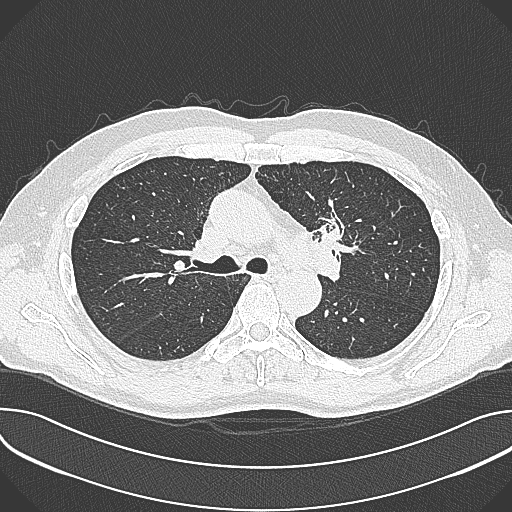
Low-dose screening chest CT, axial slice. First (baseline) screen. Lung window (W 1500 / L -600 HU). Lung (sharp) reconstruction kernel (B80f). Slice 116 of 361 in the series. 512 × 512 image matrix. Male participant, aged 59 years at enrolment. Current smoker at enrolment.
Expert-annotated lung lesion, box from (x=303, y=193) to (x=365, y=257) px. The screening reader recorded 2 non-calcified nodules or masses ≥4 mm on this exam (left upper lobe, left upper lobe); which of them this box marks is not recorded.